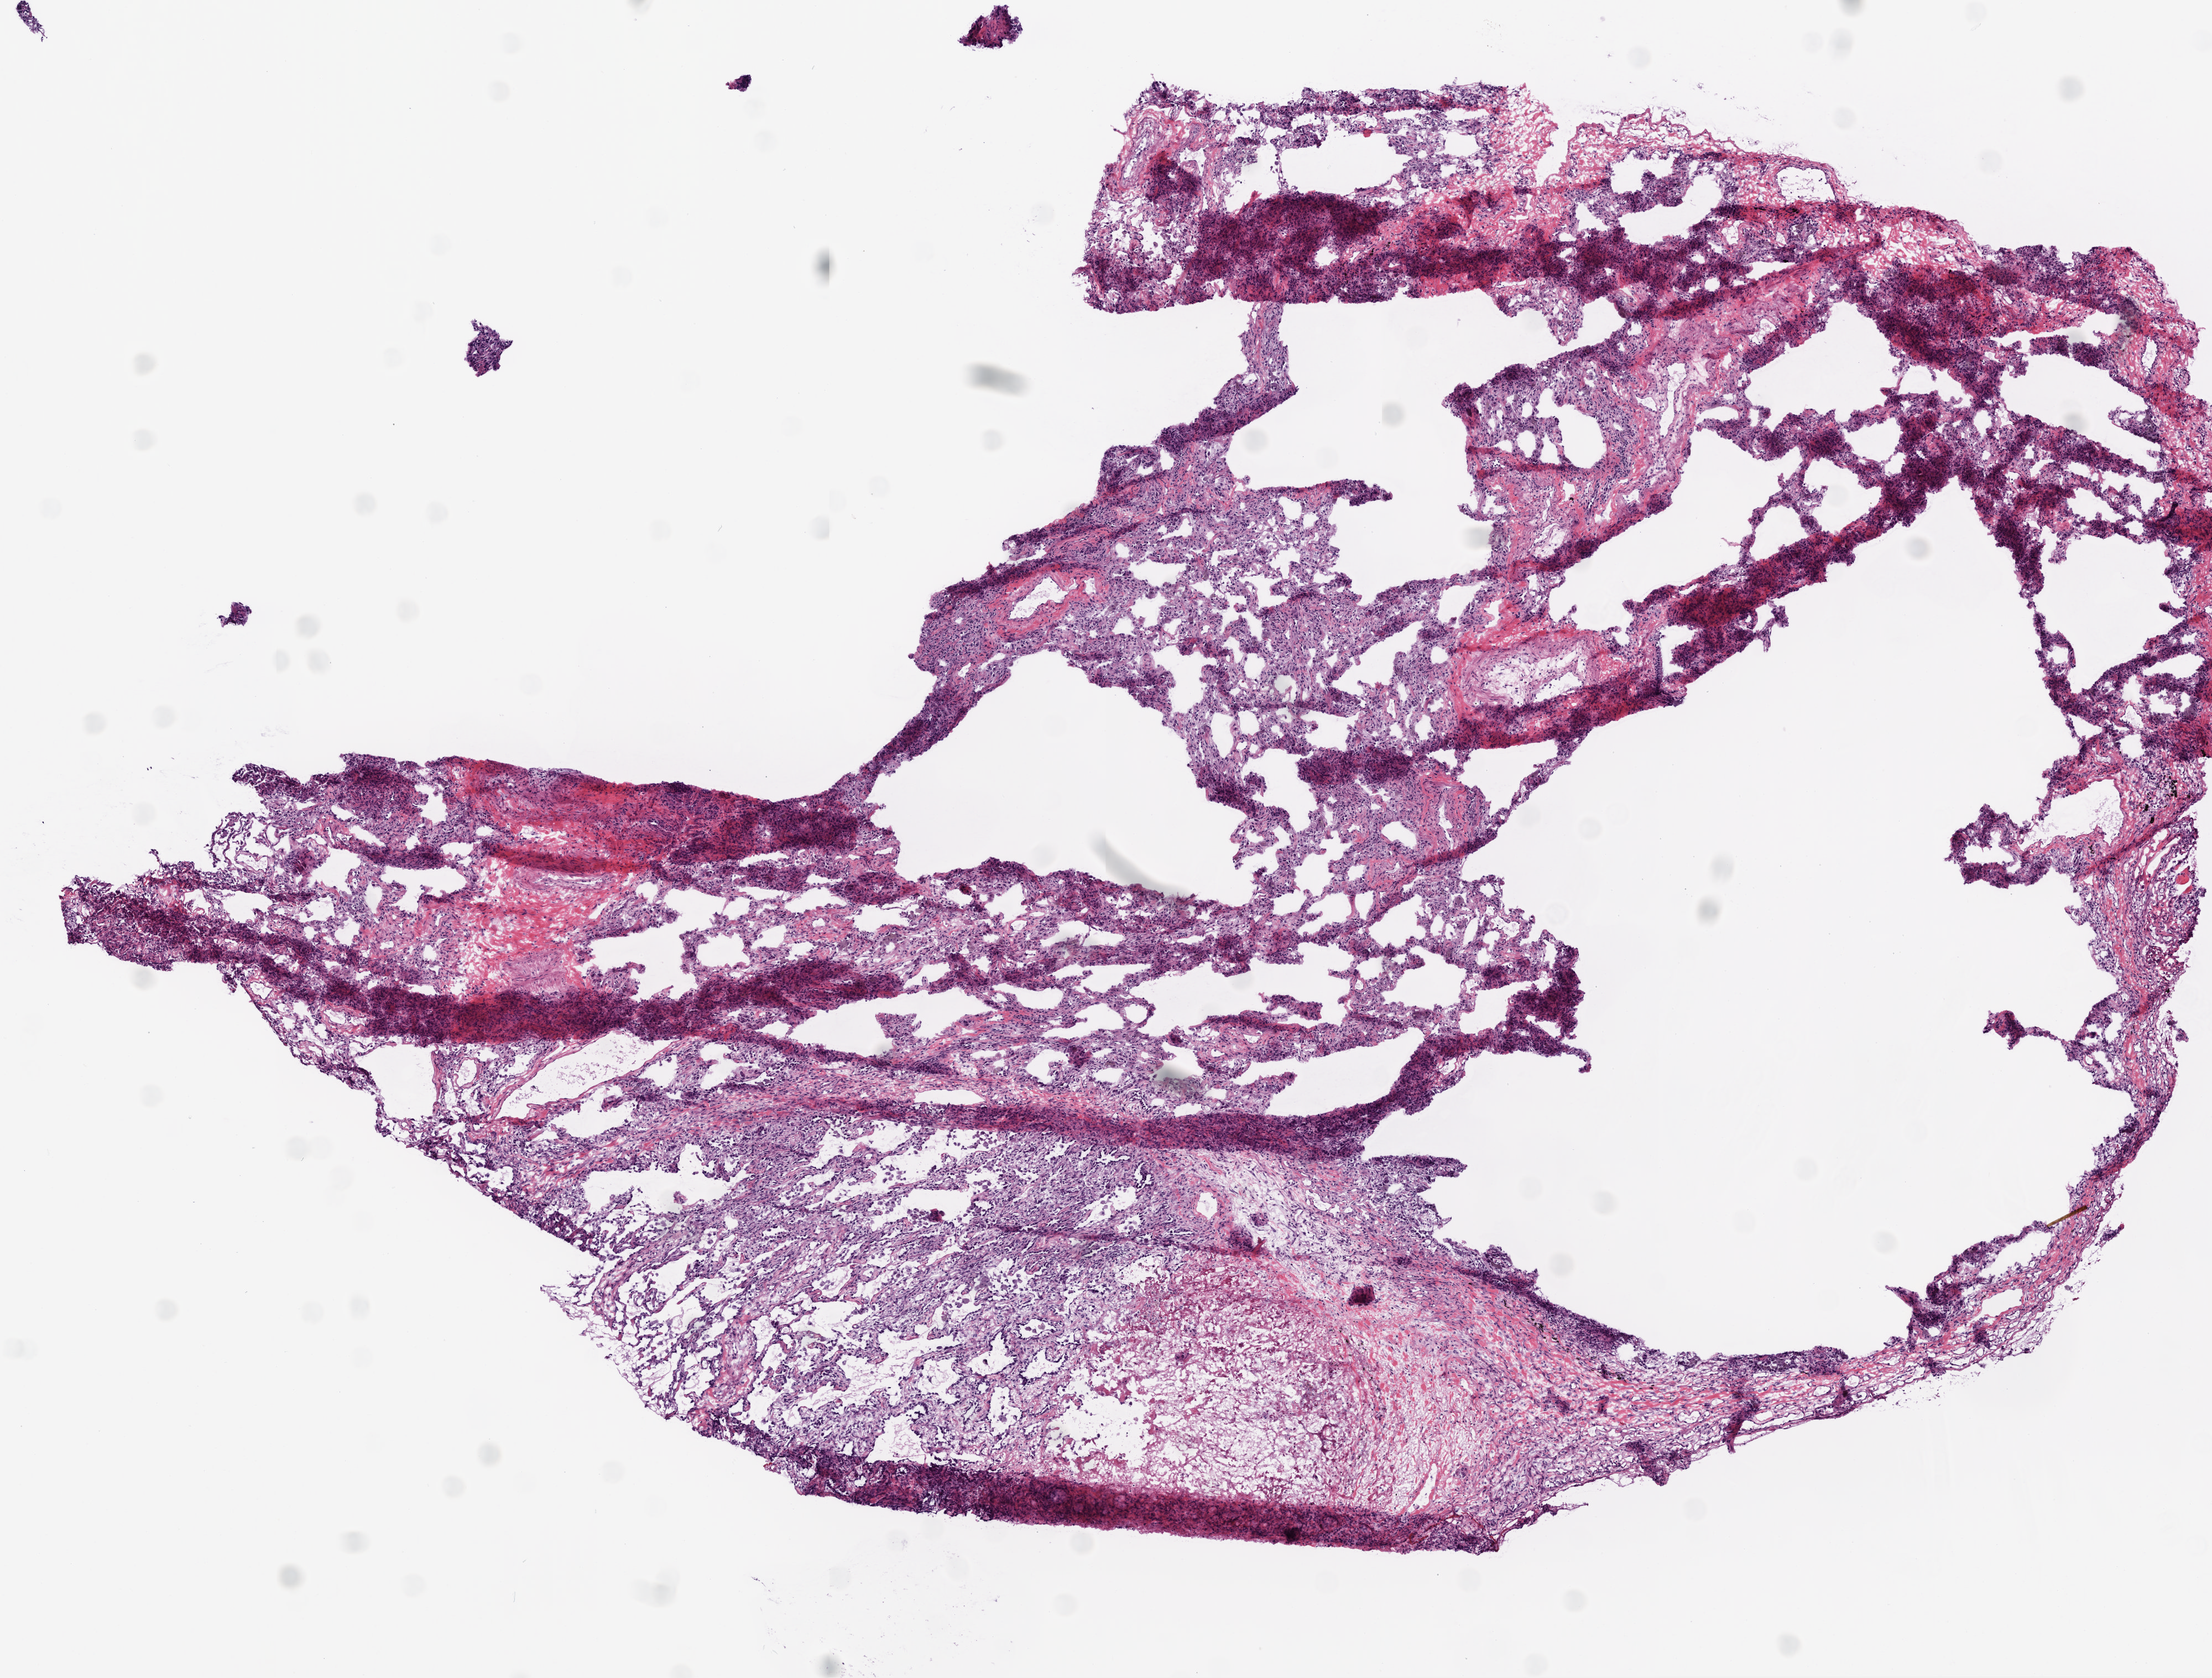
Digitized H&E-stained tissue section (whole slide), low-resolution overview of the scanned area, about 8.0 x 6.1 mm. Frozen section from the bottom of the tissue portion. Solid tissue normal (non-tumour tissue) sample from the lung. Male patient; age at initial diagnosis 58 years.
* this section: solid tissue normal sample (biorepository sample class)
* patient diagnosis: Squamous cell carcinoma, NOS (lower lobe, lung)